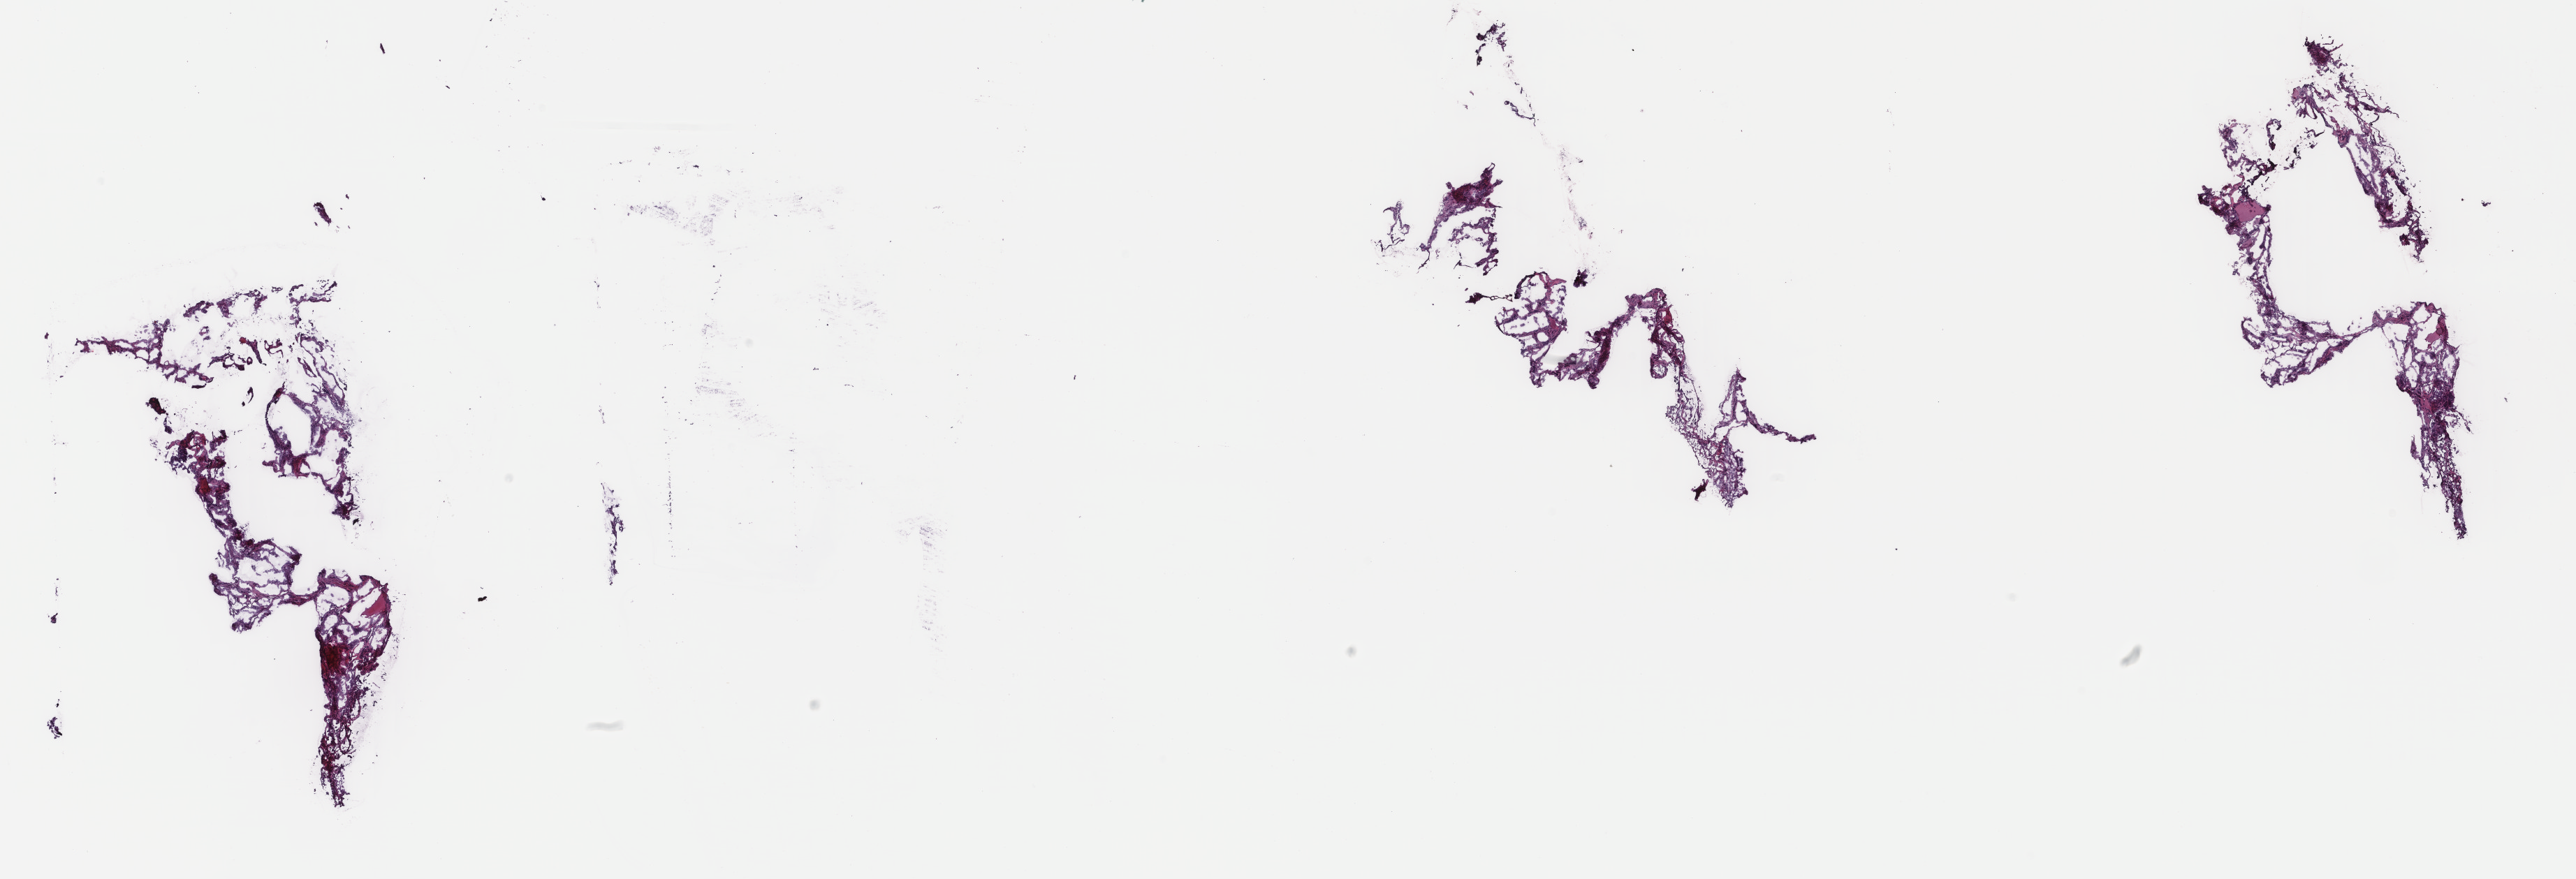
Digitized Hematoxylin and eosin (H&E) stained tissue section (whole slide), shown as a low-resolution overview of the whole scanned area (about 29.3 x 10.0 mm, from a 40x scan); frozen section from the top of the tissue portion; primary tumour sample from the thyroid. Patient: female, age at initial diagnosis 55 years. Pathologist review of this section (percent, as recorded): tumour cells 80%, tumour nuclei 100%, normal cells 0%, stromal cells 20%, necrosis 0%. Infiltration values recorded for this section: lymphocyte infiltration 0%, monocyte infiltration 1%, neutrophil infiltration 0%.
AJCC pathologic stage: III. Laterality: right. Diagnosis: Papillary adenocarcinoma, NOS (thyroid gland). TNM: T2 N1 M0.